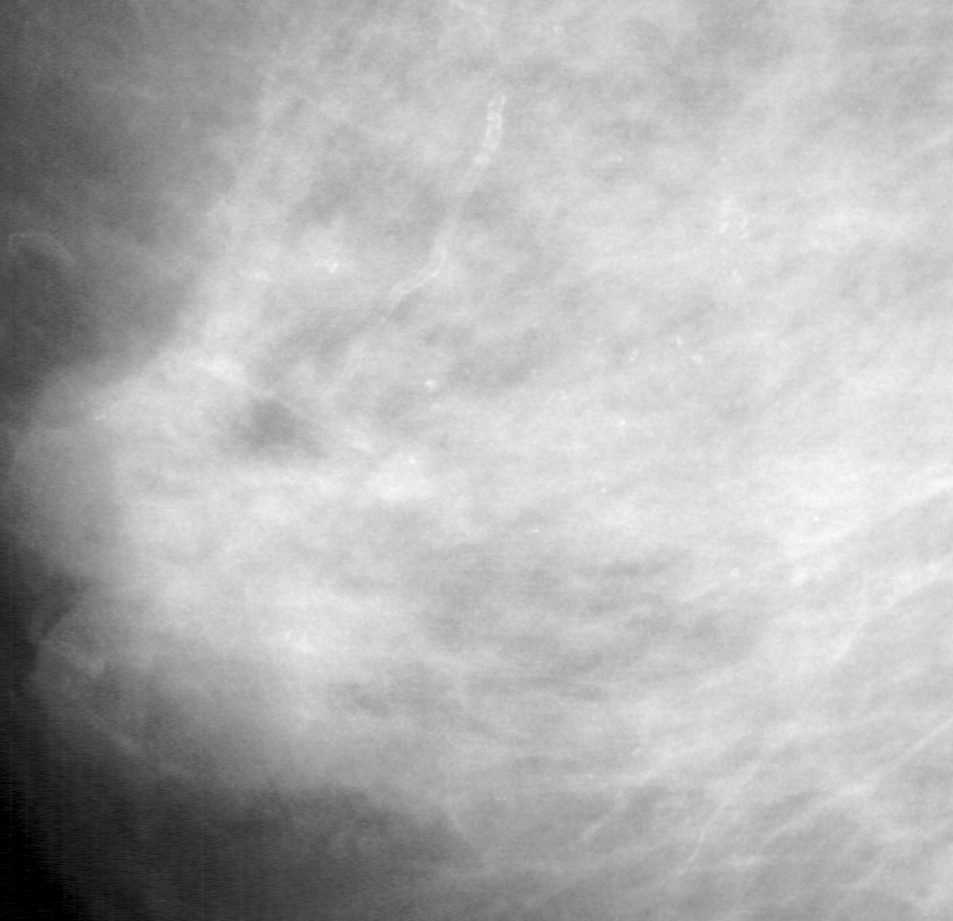
Cropped region of a digitized screen-film mammogram centred on a radiologist-marked abnormality, left breast, MLO view, BI-RADS breast density category 4 (scale 1–4).
Calcifications, morphology punctate / amorphous, distribution regional; BI-RADS assessment category 4; subtlety rating 3 on a 1 (subtle) to 5 (obvious) scale; pathology (as recorded): benign.